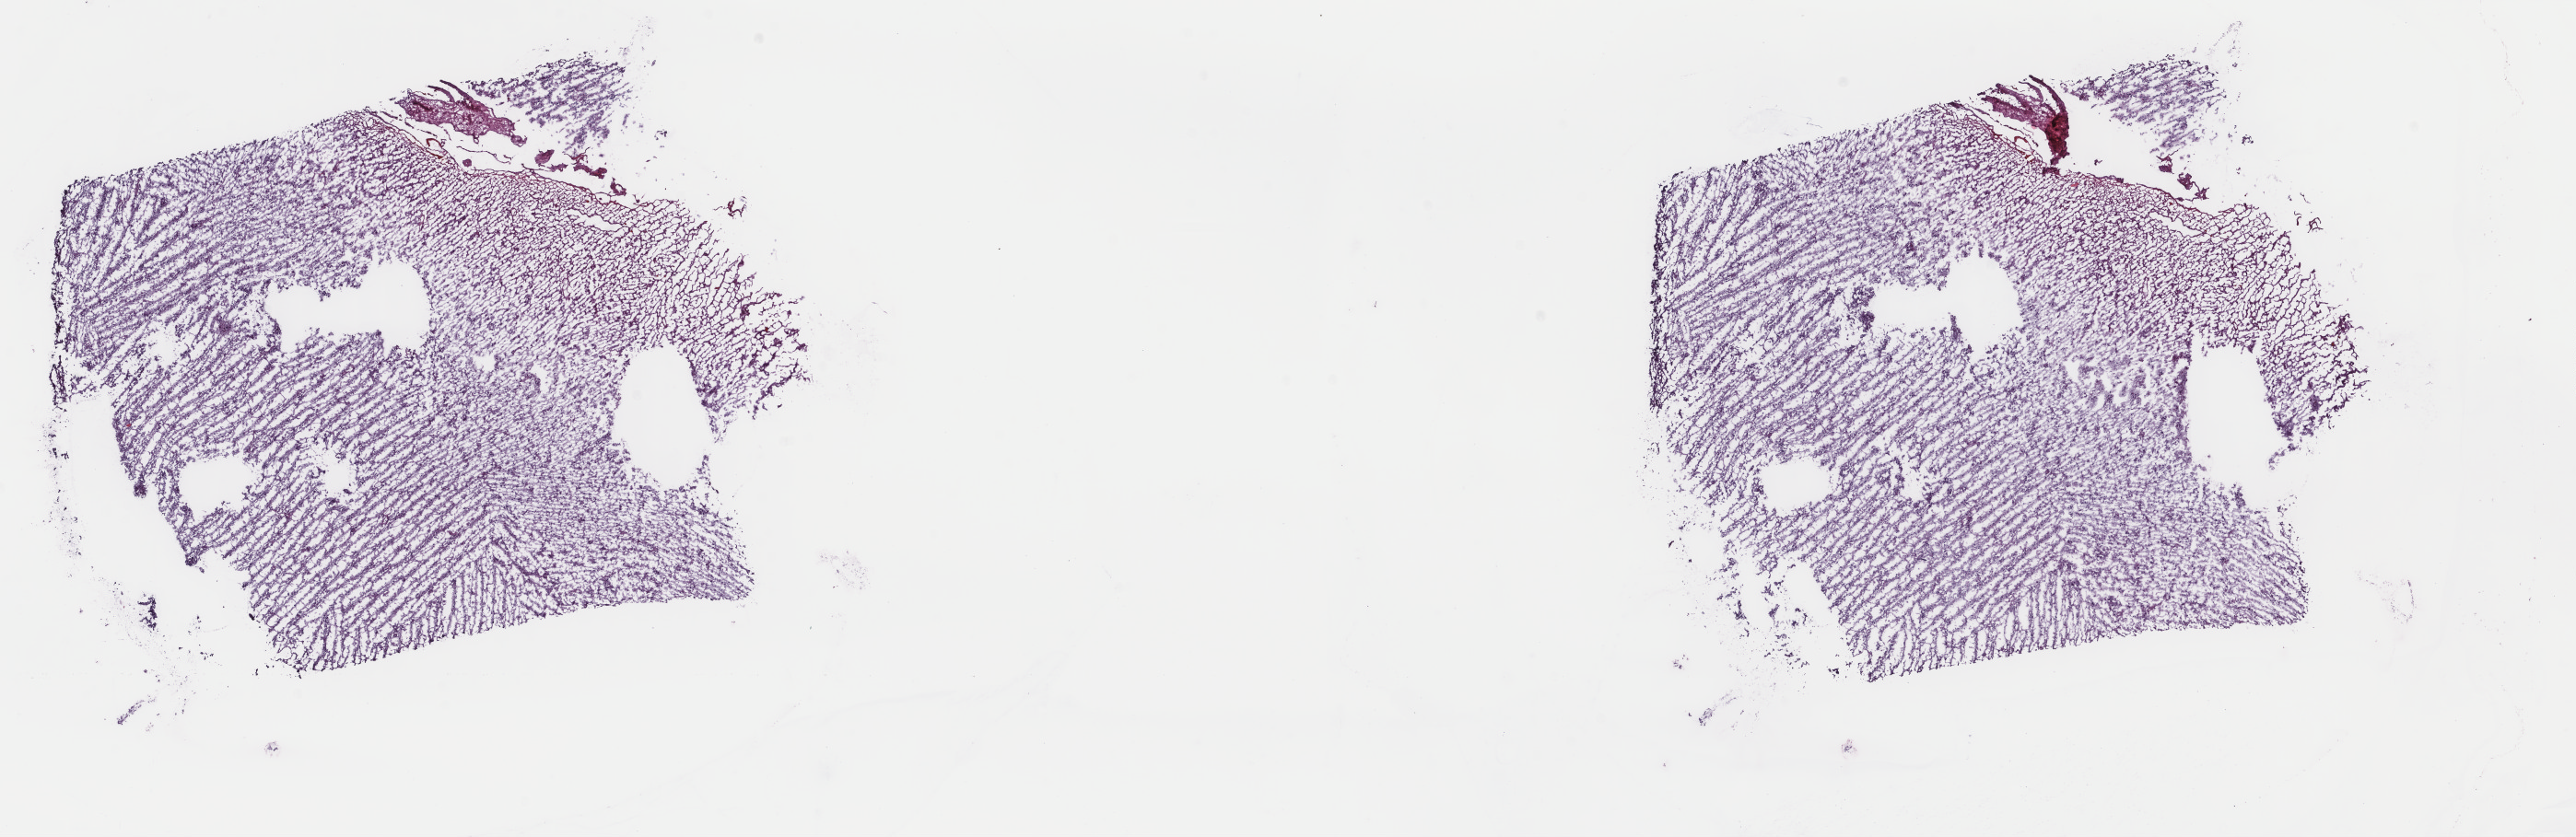
Whole-slide histology image, H&E — shown as a low-resolution overview of the whole scanned area (about 22.2 x 7.2 mm, slide scanned at 40x). Frozen section from the top of the tissue portion. Sample: primary tumour, brain. Female, age 41 years at initial diagnosis. Slide review estimates, as recorded: tumour cells 75%, tumour nuclei 80%.
Pathologic diagnosis: Astrocytoma, anaplastic (frontal lobe).